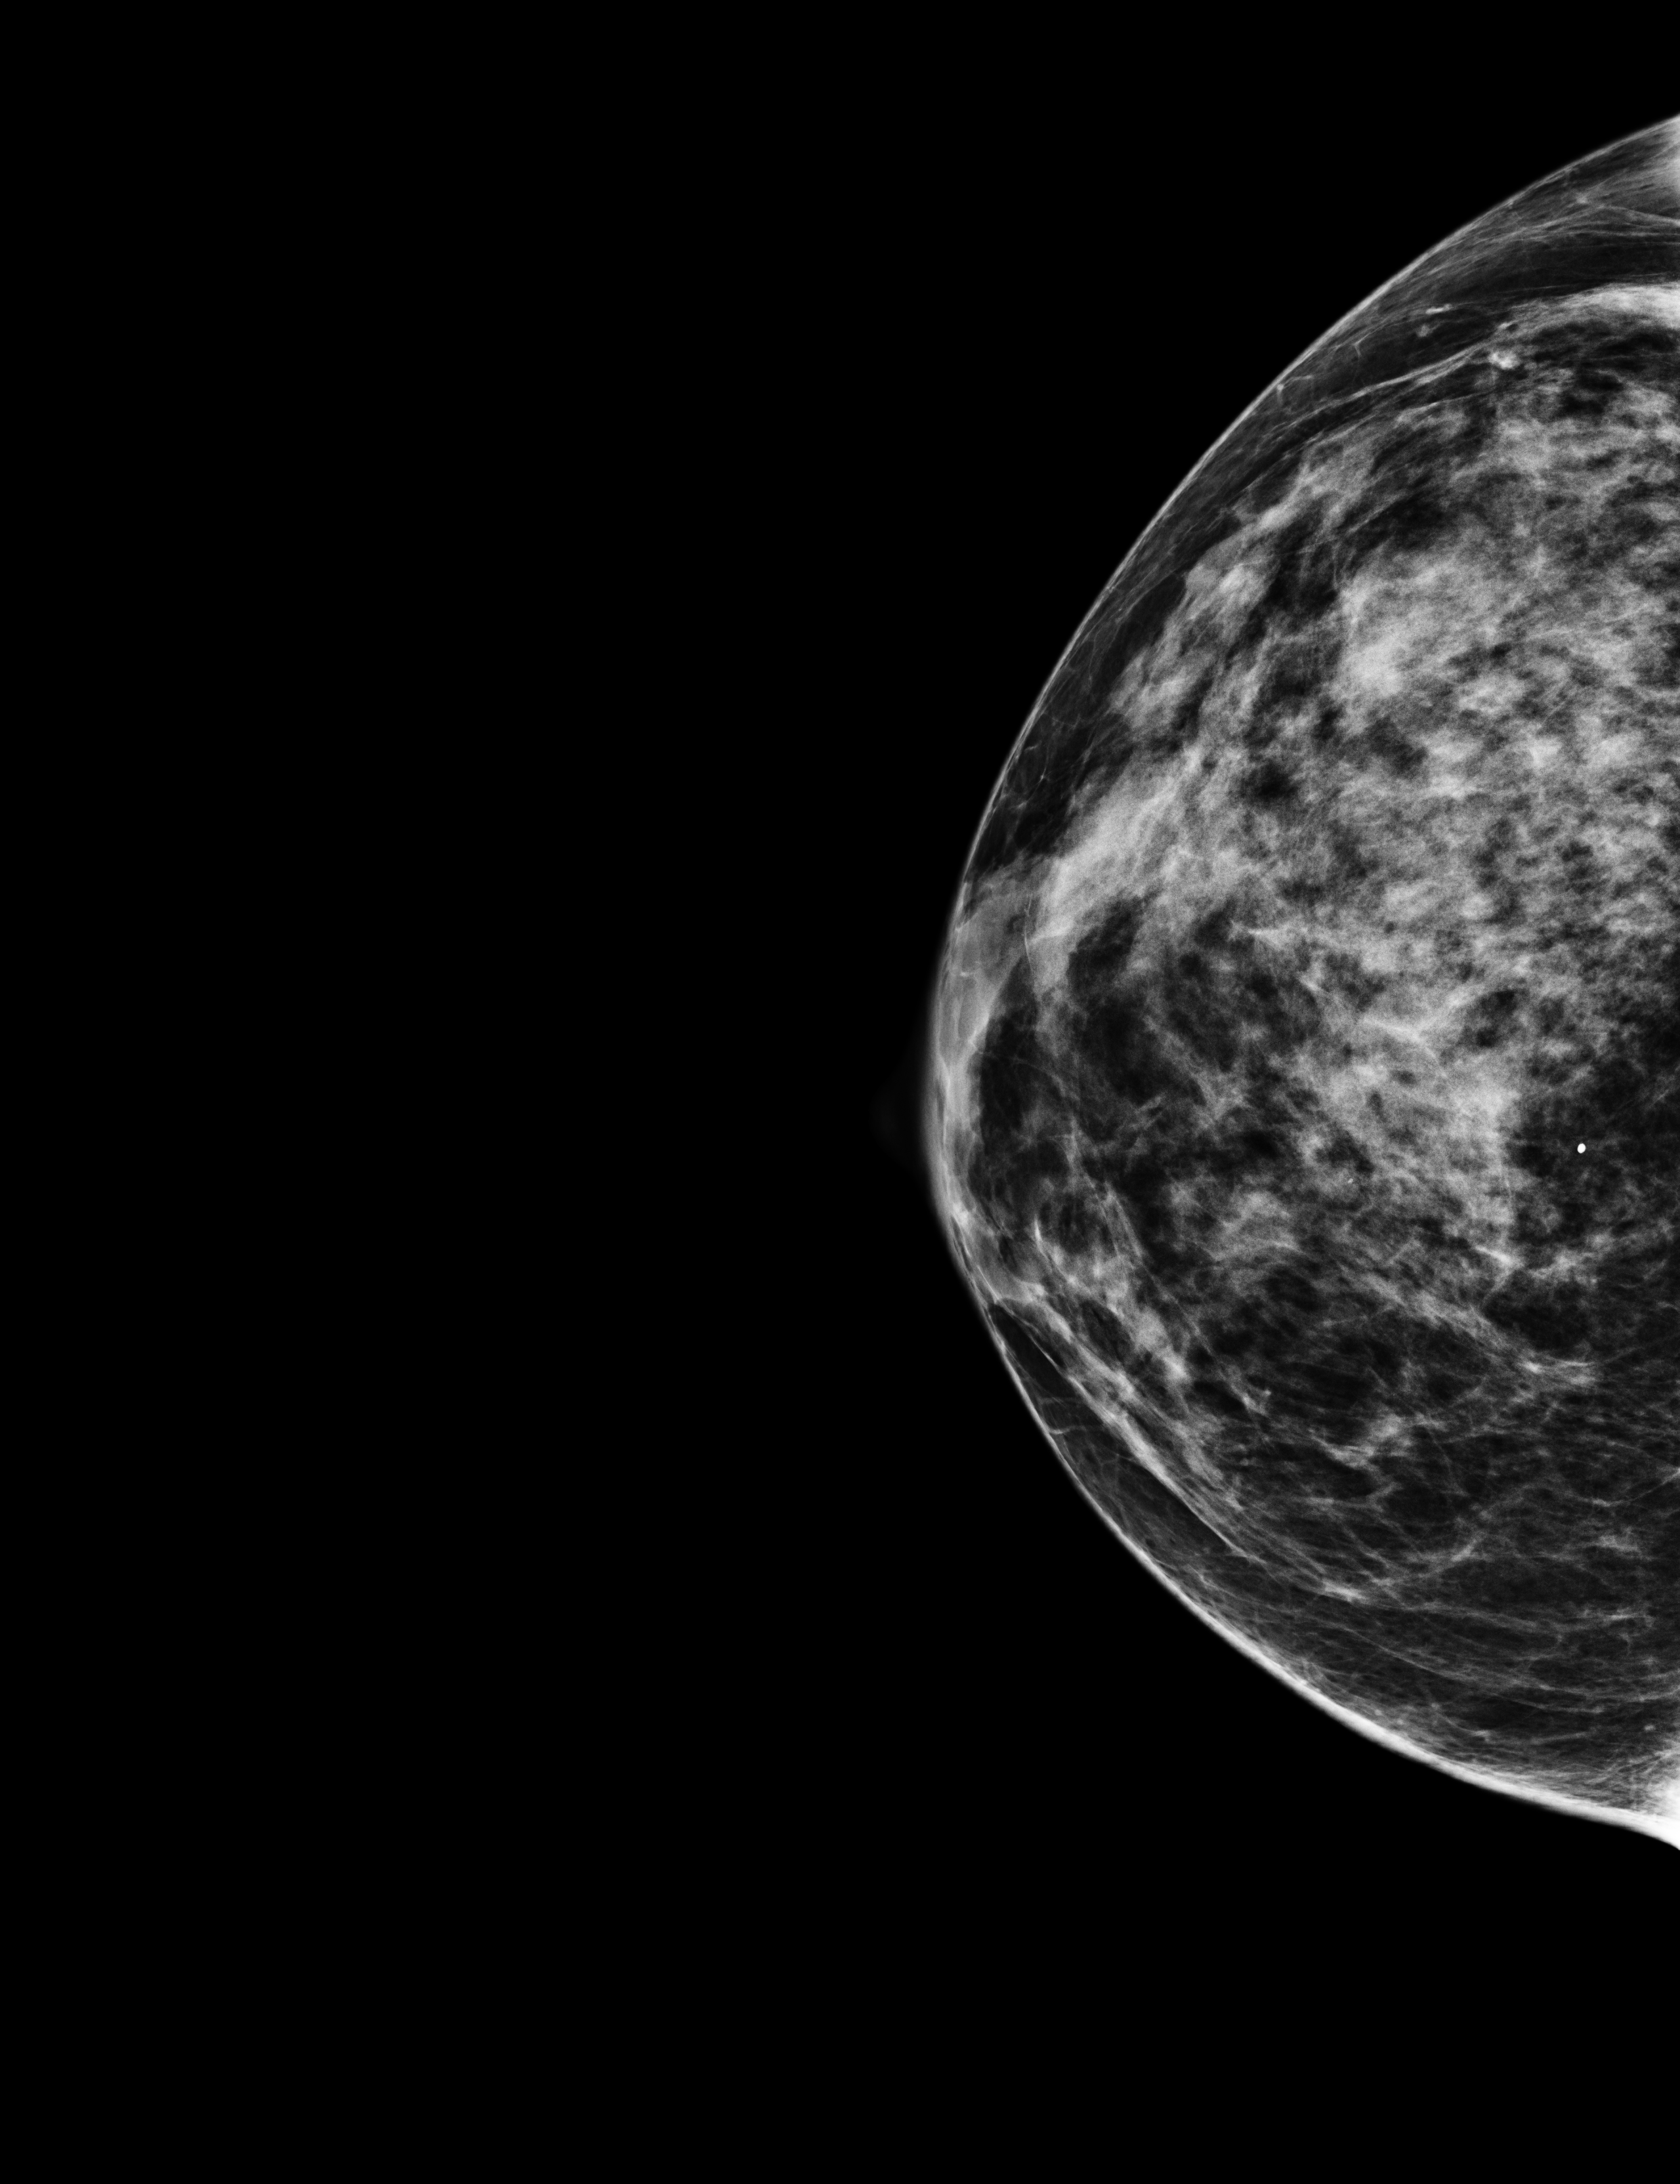
Screening examination, compressed breast thickness 54 mm, system: Selenia Dimensions.
Image type: full-field digital mammogram. Breast: right. Projection: cranio-caudal projection.